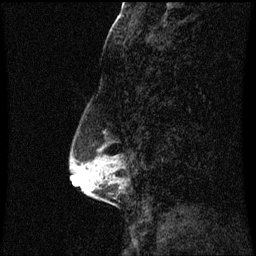
Breast MRI (dynamic contrast-enhanced), one sagittal slice. Position 20 of 60 along the scan axis. Dynamic contrast-enhanced series, image 2 of 3 at this slice position (ordered by acquisition). 1.5 T. TE 4.2 ms, TR 8.9 ms. 2 mm slice thickness. 256 × 256 image matrix. Patient: female, 50 years. From the clinical record (not read from this slice): setting: breast cancer imaged before/during neoadjuvant chemotherapy; receptor status: triple-negative.
Annotated regions visible in this slice (semi-automatically segmented with operator editing):
- analysis volume of interest (the breast-tissue region the enhancement analysis was run in; not a lesion): bounding box <71,134,118,205> (left, top, right, bottom; pixels)
- tumour enhancement mask (voxels above the 70 % enhancement threshold inside the analysis volume of interest): <89,162,104,167>